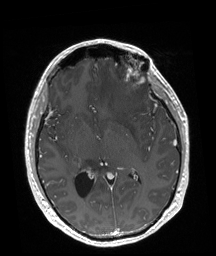
Brain MRI from a brain-tumour surgery series, one axial slice; position 95 of 192 along the scan axis; T1-weighted post-contrast; 1 mm slice thickness; 216 × 256 image matrix, field of view 219 × 260 mm.
Structures marked on this image (manually delineated by an expert):
- tumour: box from (x=124, y=58) to (x=144, y=89) px